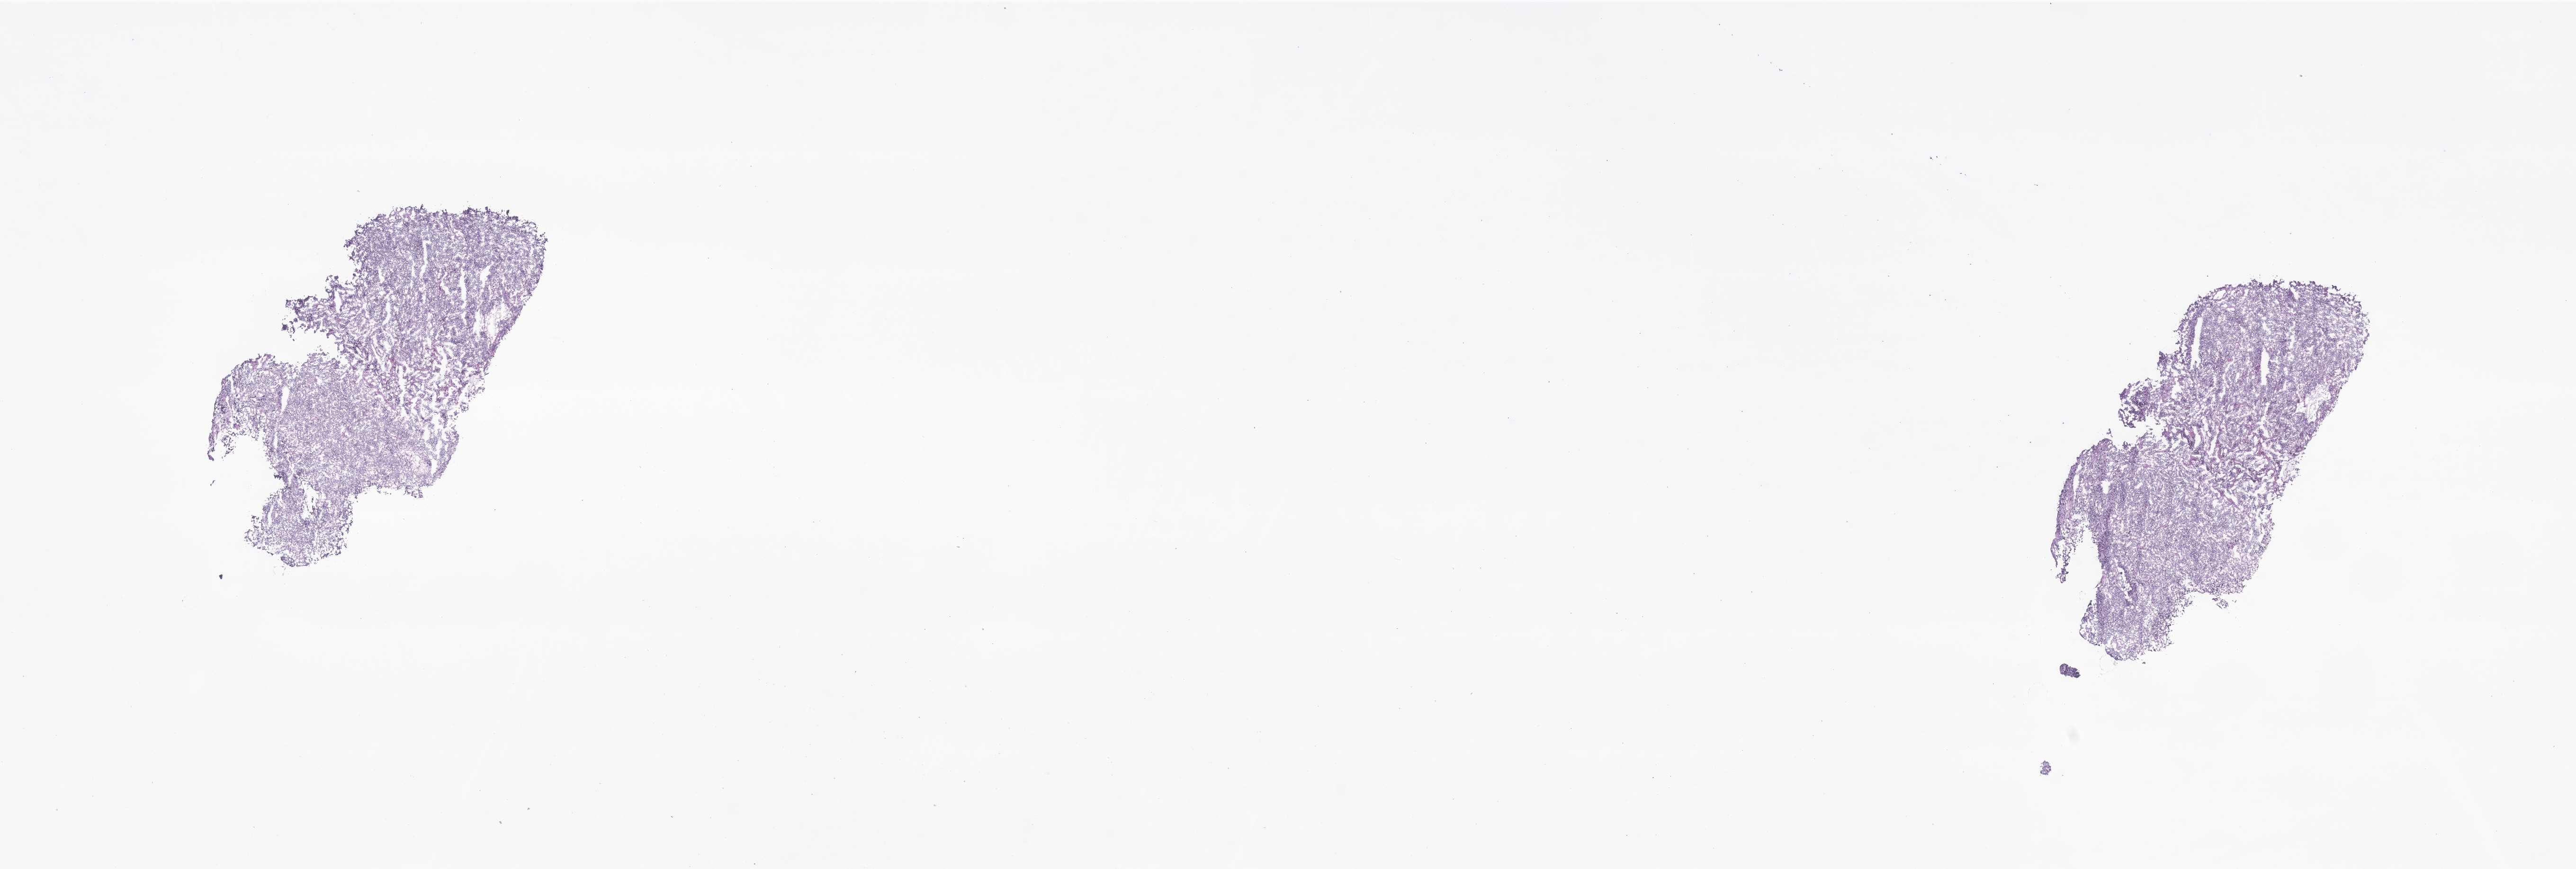
Whole-slide image, hematoxylin and eosin (H&E) stain of tumor tissue from the brain — low-resolution overview of the scanned area, about 22.9 x 7.7 mm; frozen section. Patient: male, age 96 months.
Recorded diagnosis: Medulloblastoma, NOS.